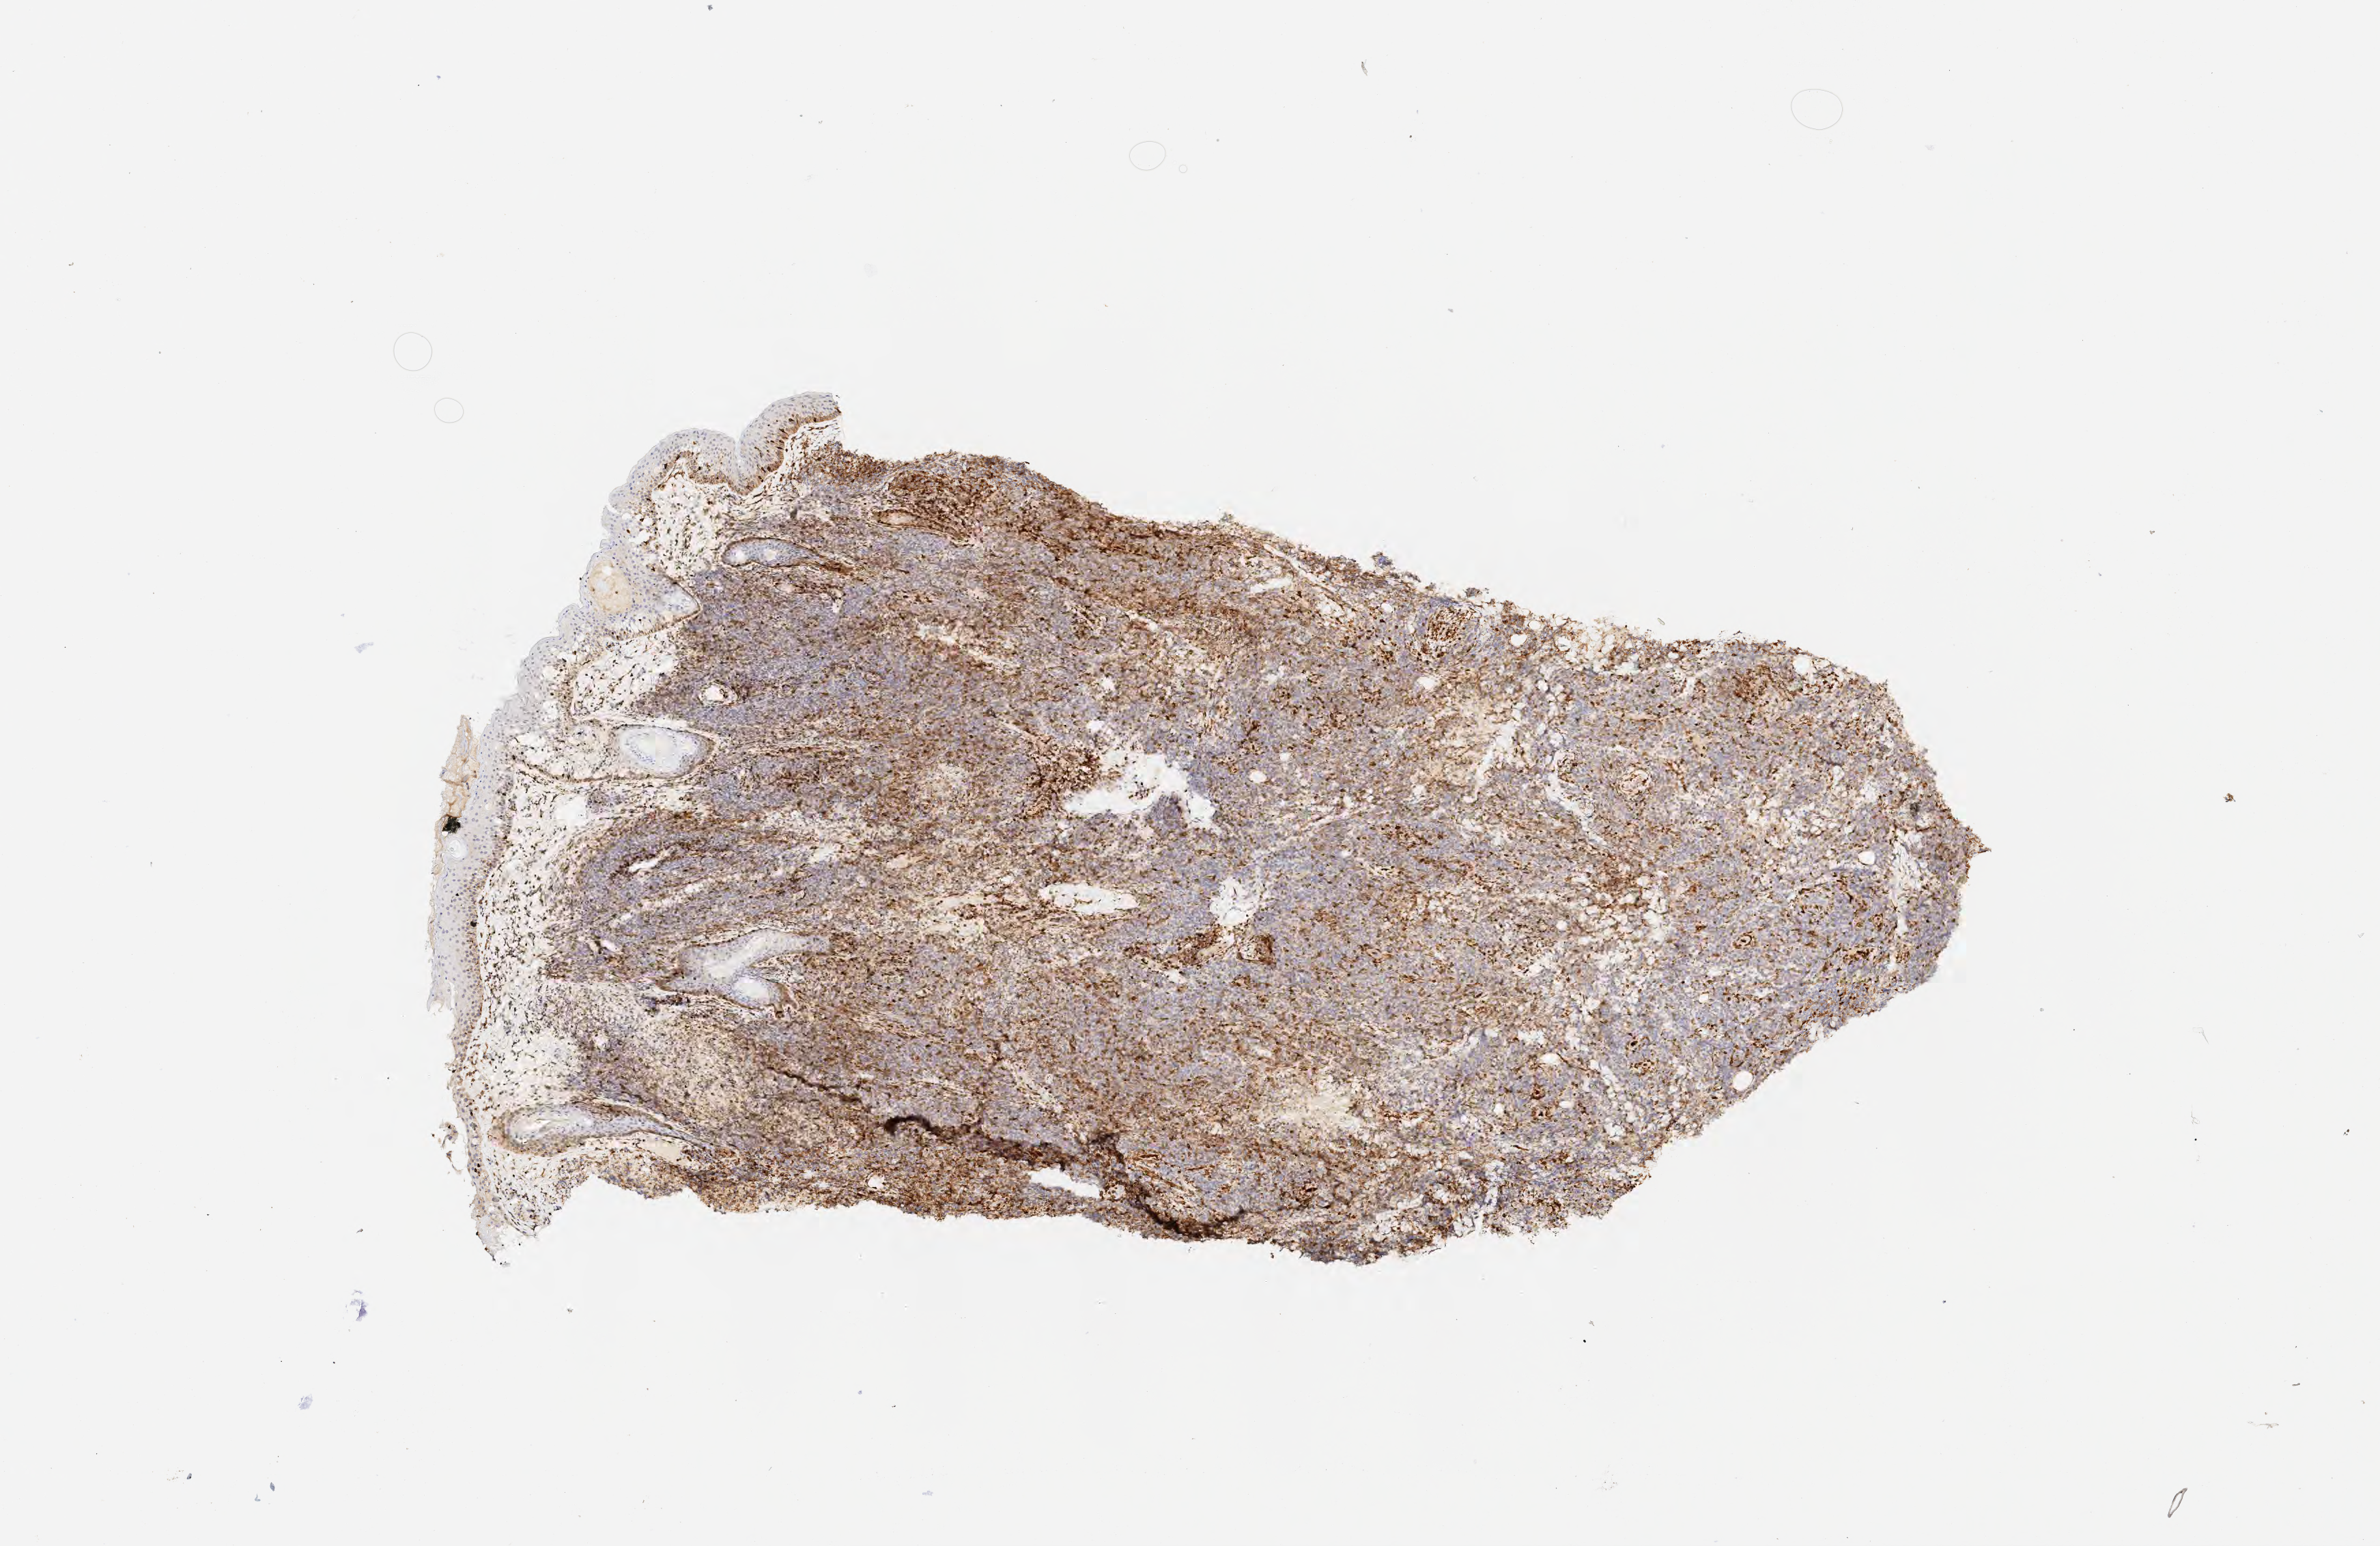
Immunohistochemistry (IHC) whole-slide image stained for BCL2 — low-resolution overview of the scanned area, about 7.0 x 4.6 mm, tumor tissue. Male patient, aged 41.
Diagnosis: Diffuse large B-cell lymphoma, NOS.